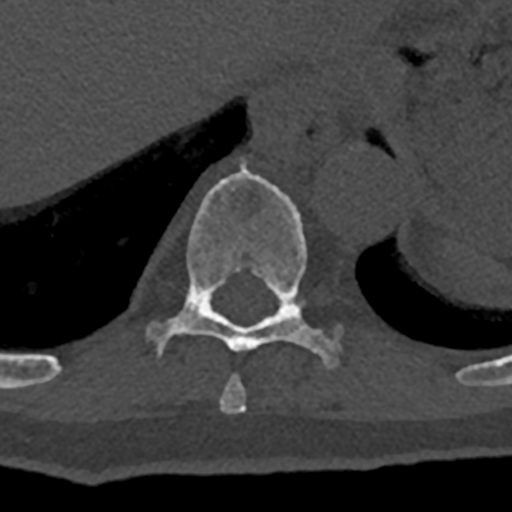
CT including the spine, one axial slice. Position 602 of 797 along the scan axis. Bone window (W 1800 / L 400 HU). 512 × 512 image matrix, field of view 160 × 160 mm. Male patient, age 74 years. Case-level facts recorded for this patient, not image findings: primary cancer: renal.
Structures marked on this image (semi-automatically segmented with operator editing):
- T10 vertebra: box from (x=147, y=158) to (x=341, y=368) px
- T11 vertebra: (x=286, y=299)–(x=302, y=306)
- T9 vertebra: (x=219, y=374)–(x=247, y=413)